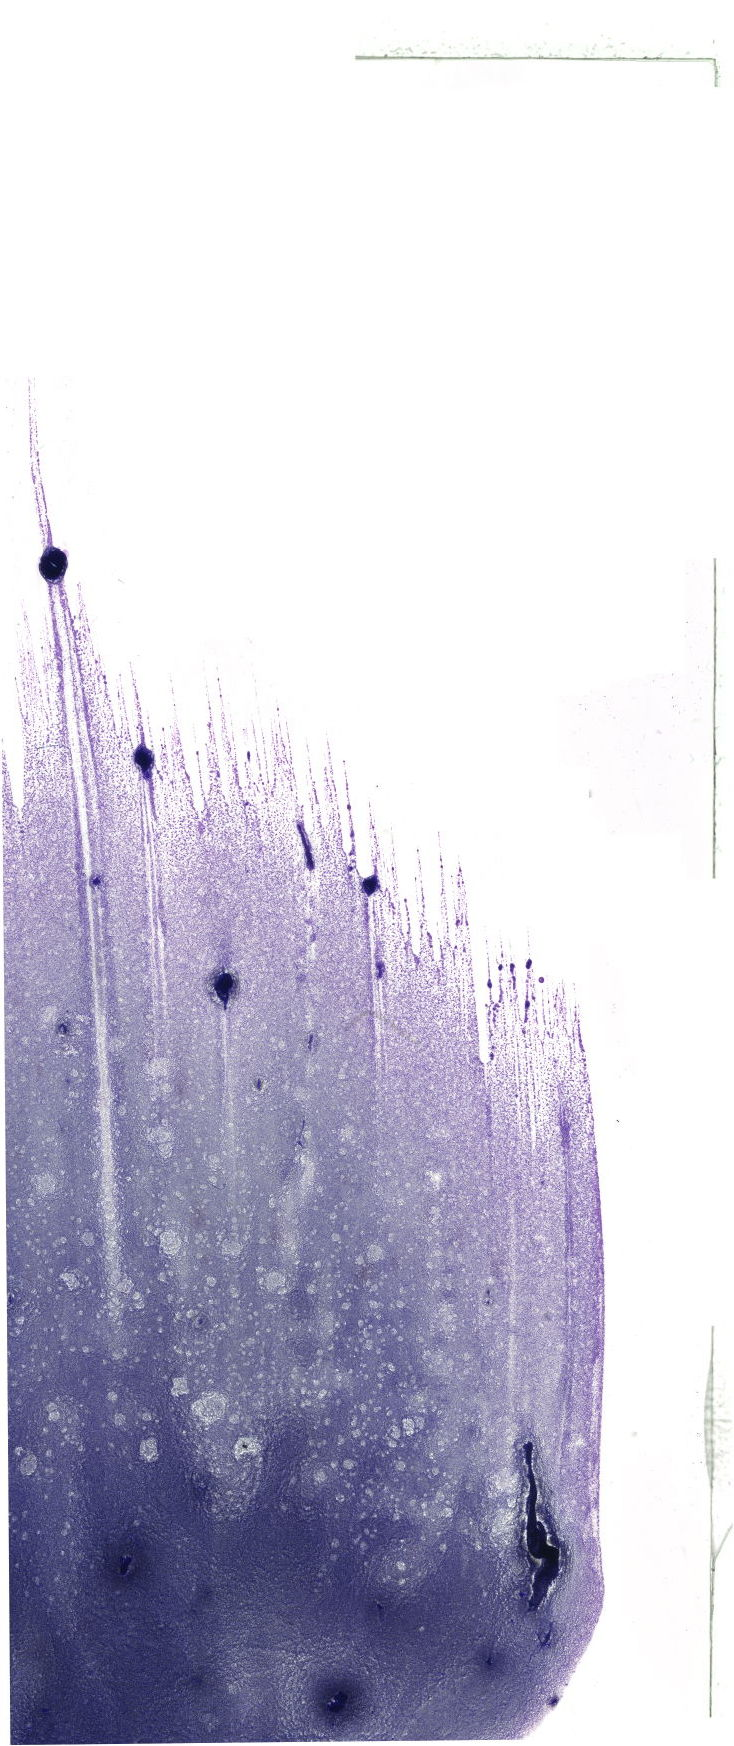
May-Grünwald–Giemsa-stained marrow aspirate smear (whole slide), low-resolution overview of the scanned area, about 20.8 x 49.5 mm. Patient sex: female.
• diagnosis: Chronic Phase Chronic Myeloid Leukemia, BCR-ABL1 Positive